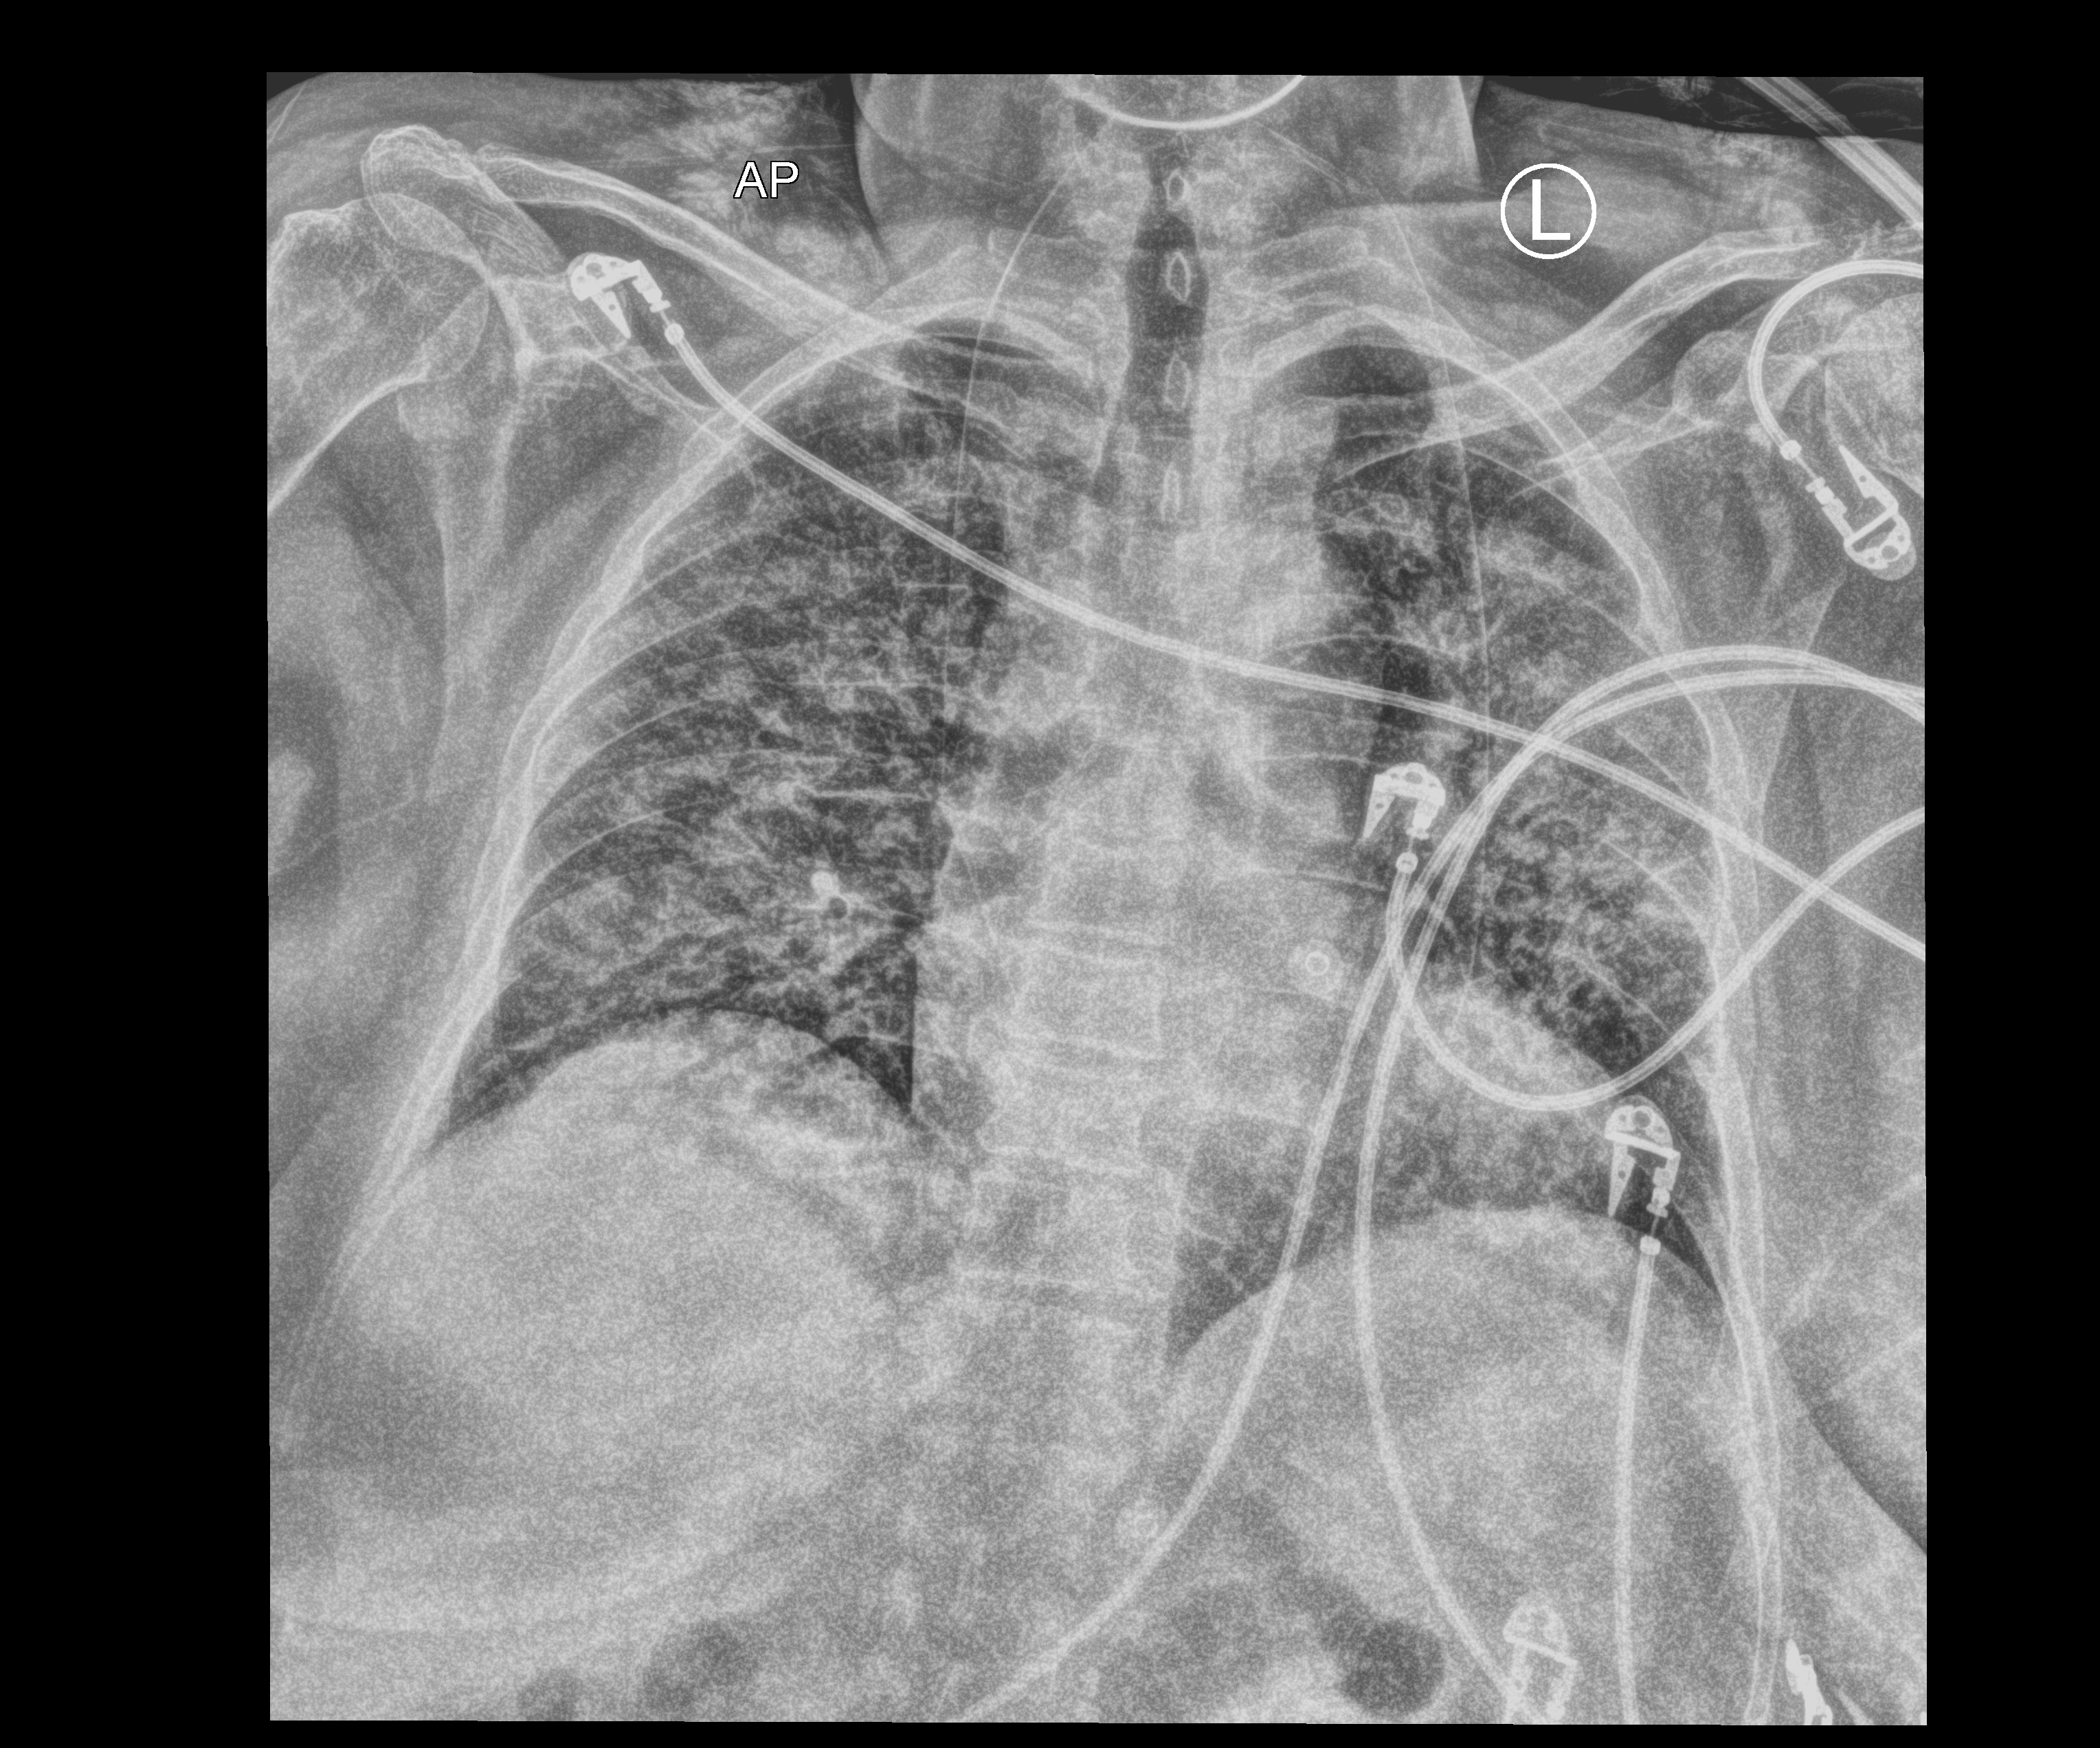
Bedside chest radiograph (computed radiography), anteroposterior (AP) projection. Patient hospitalised with COVID-19; female, aged 60–74 years.
Admission-level facts for this patient (not findings on this image; timing relative to this image not recorded):
- admitted to intensive care during this hospital stay: yes
- hypertension (admission record): yes
- mechanically ventilated during this hospital stay: no